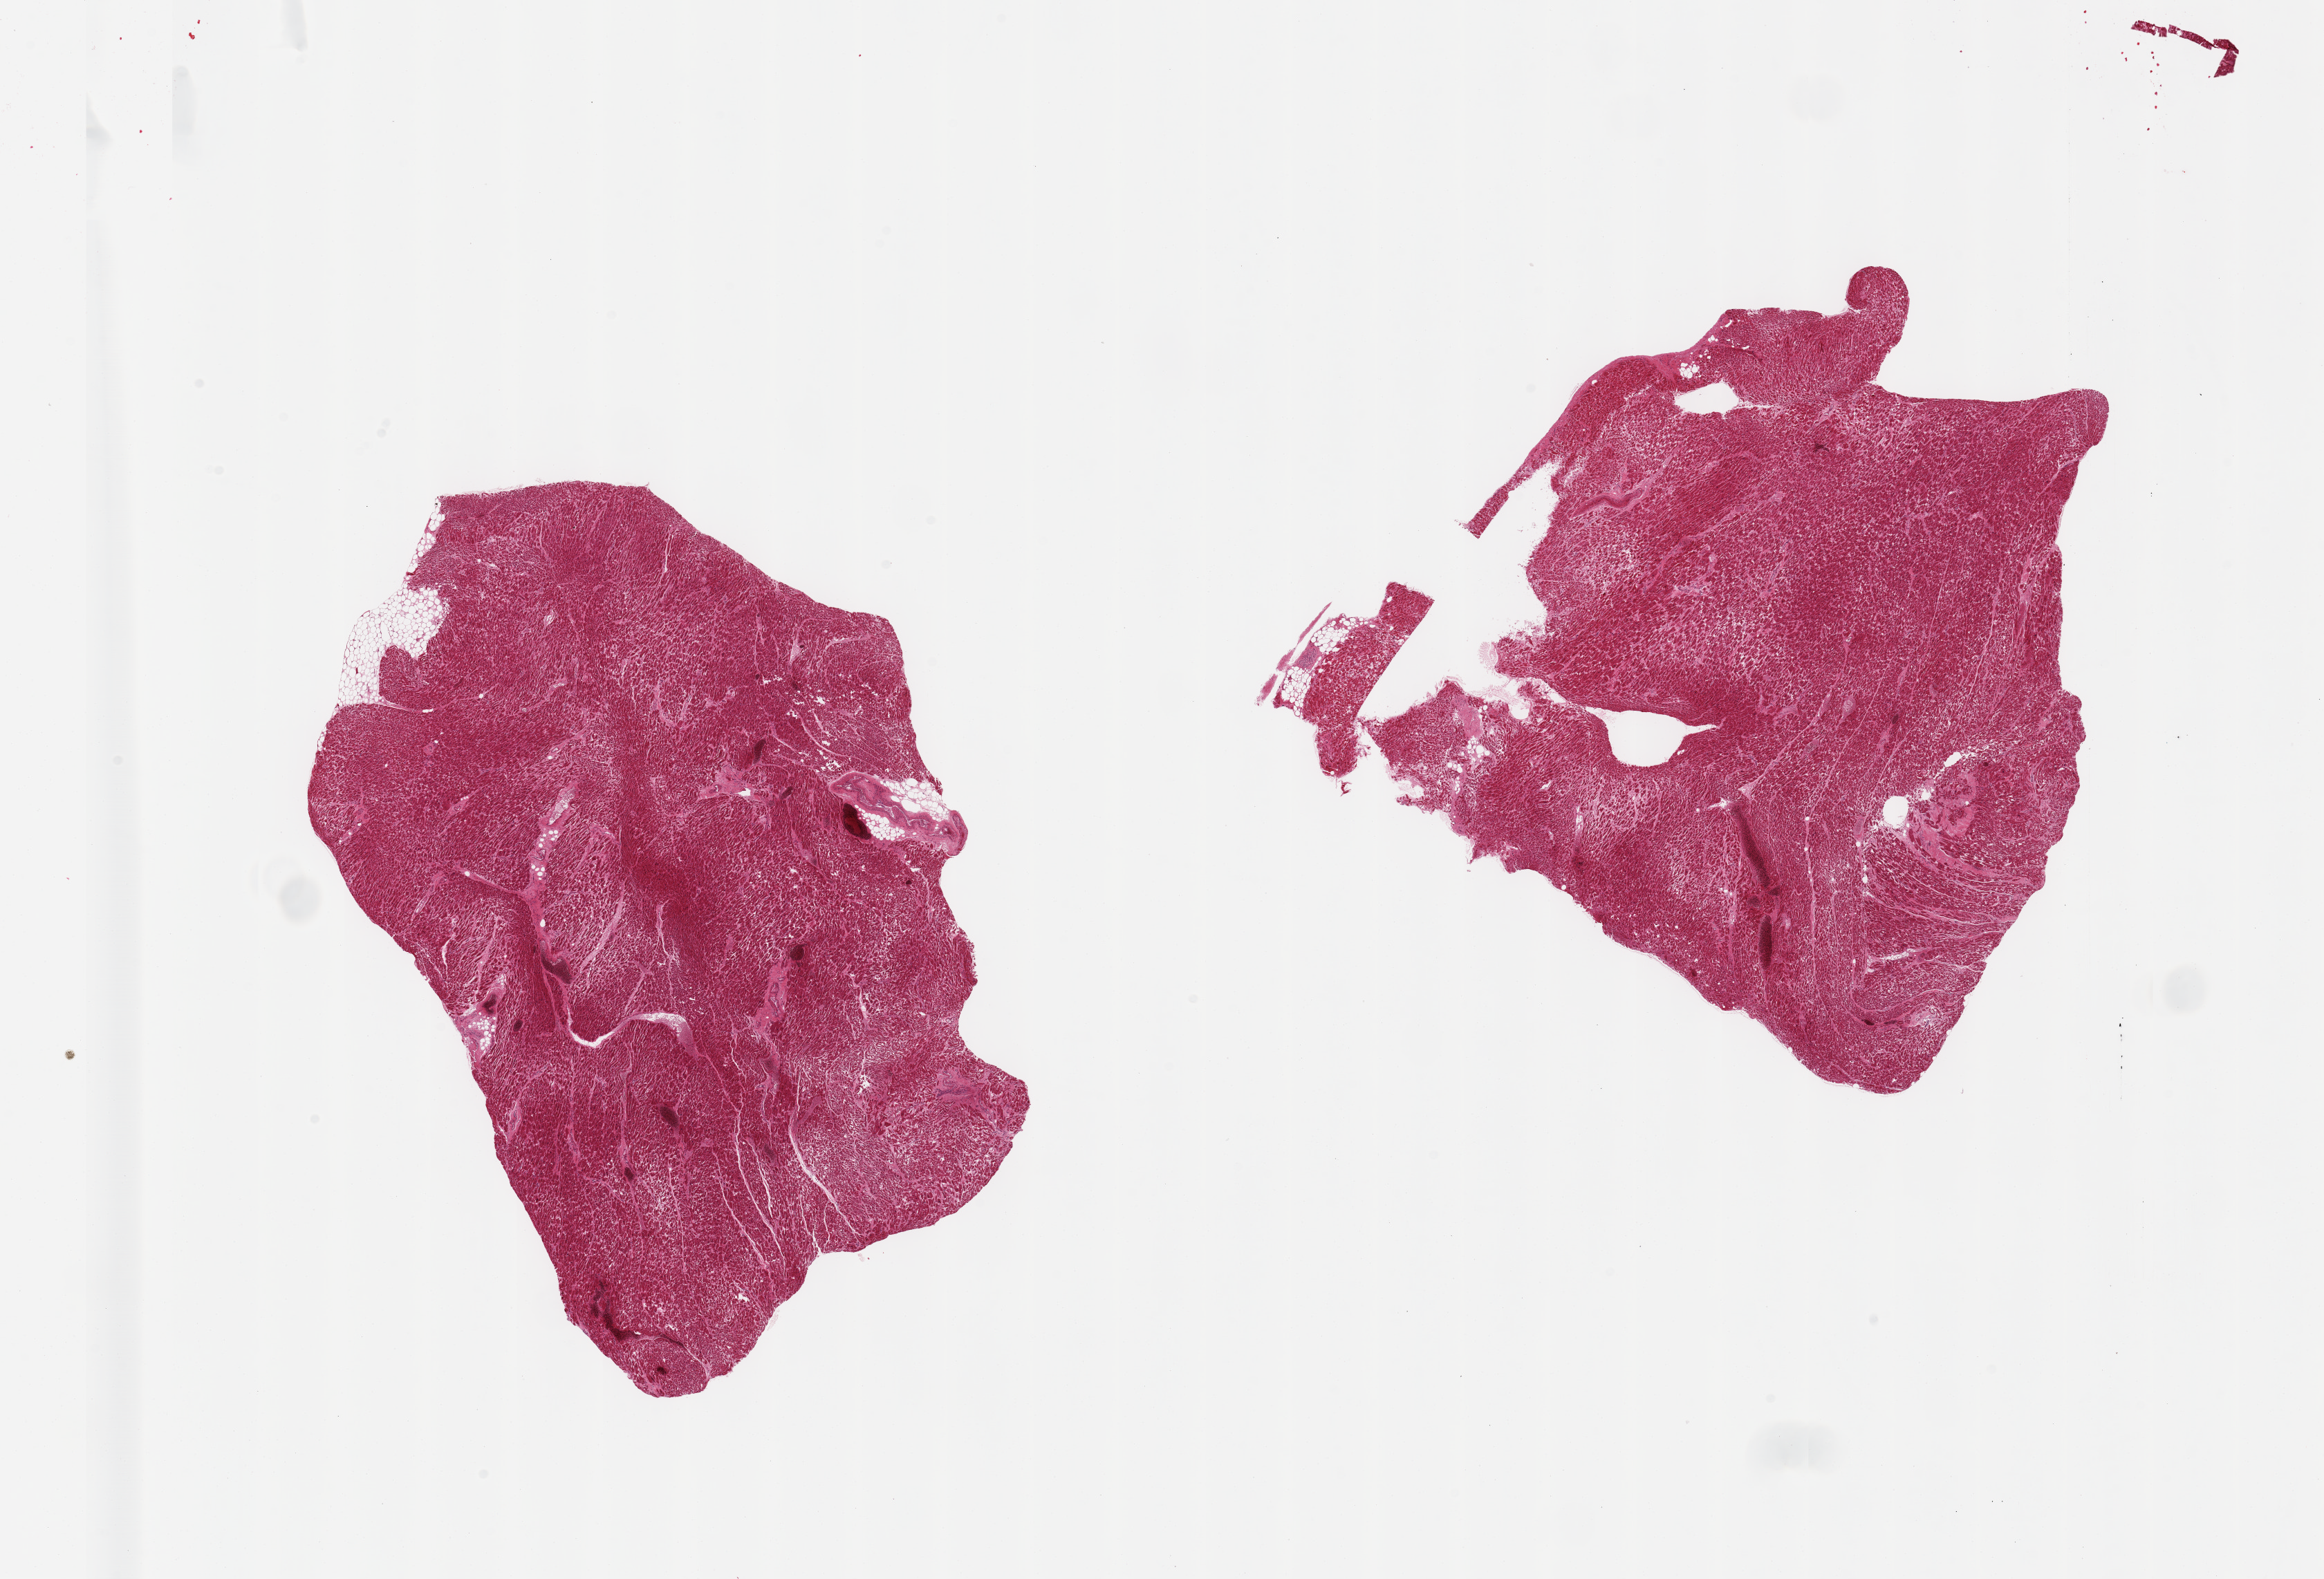
Haematoxylin and eosin whole-slide image — low-resolution overview of the scanned area, about 26.6 x 18.1 mm. PAXgene-fixed paraffin-embedded (PFPE) section. Section of heart (target tissue). Tissue donor sample. Male donor.
Reviewer comment on this tissue sample: 2 pieces; interstitial fibrosis and focal scarring.